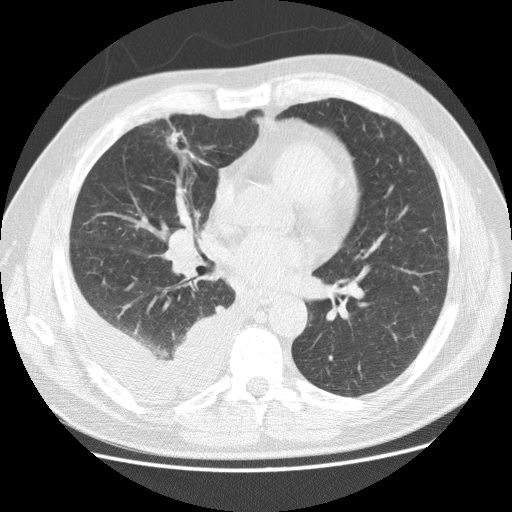
Low-dose screening chest CT, axial slice; baseline screening round; lung window (W 1500 / L -600 HU); standard (soft-tissue) reconstruction kernel (STANDARD); 120 kVp; slice 81 of 142 in the series; 512 × 512 image matrix. Male participant, aged 65 years at enrolment.
Expert-annotated lung lesion, bounding box (x1, y1, x2, y2) in pixels: (149, 121, 215, 177). Screening reader's record for this exam (one nodule recorded; not confirmed to be the boxed lesion): non-calcified nodule or mass ≥4 mm, right middle lobe, 22 × 15 mm, spiculated (stellate) margins, mixed attenuation.